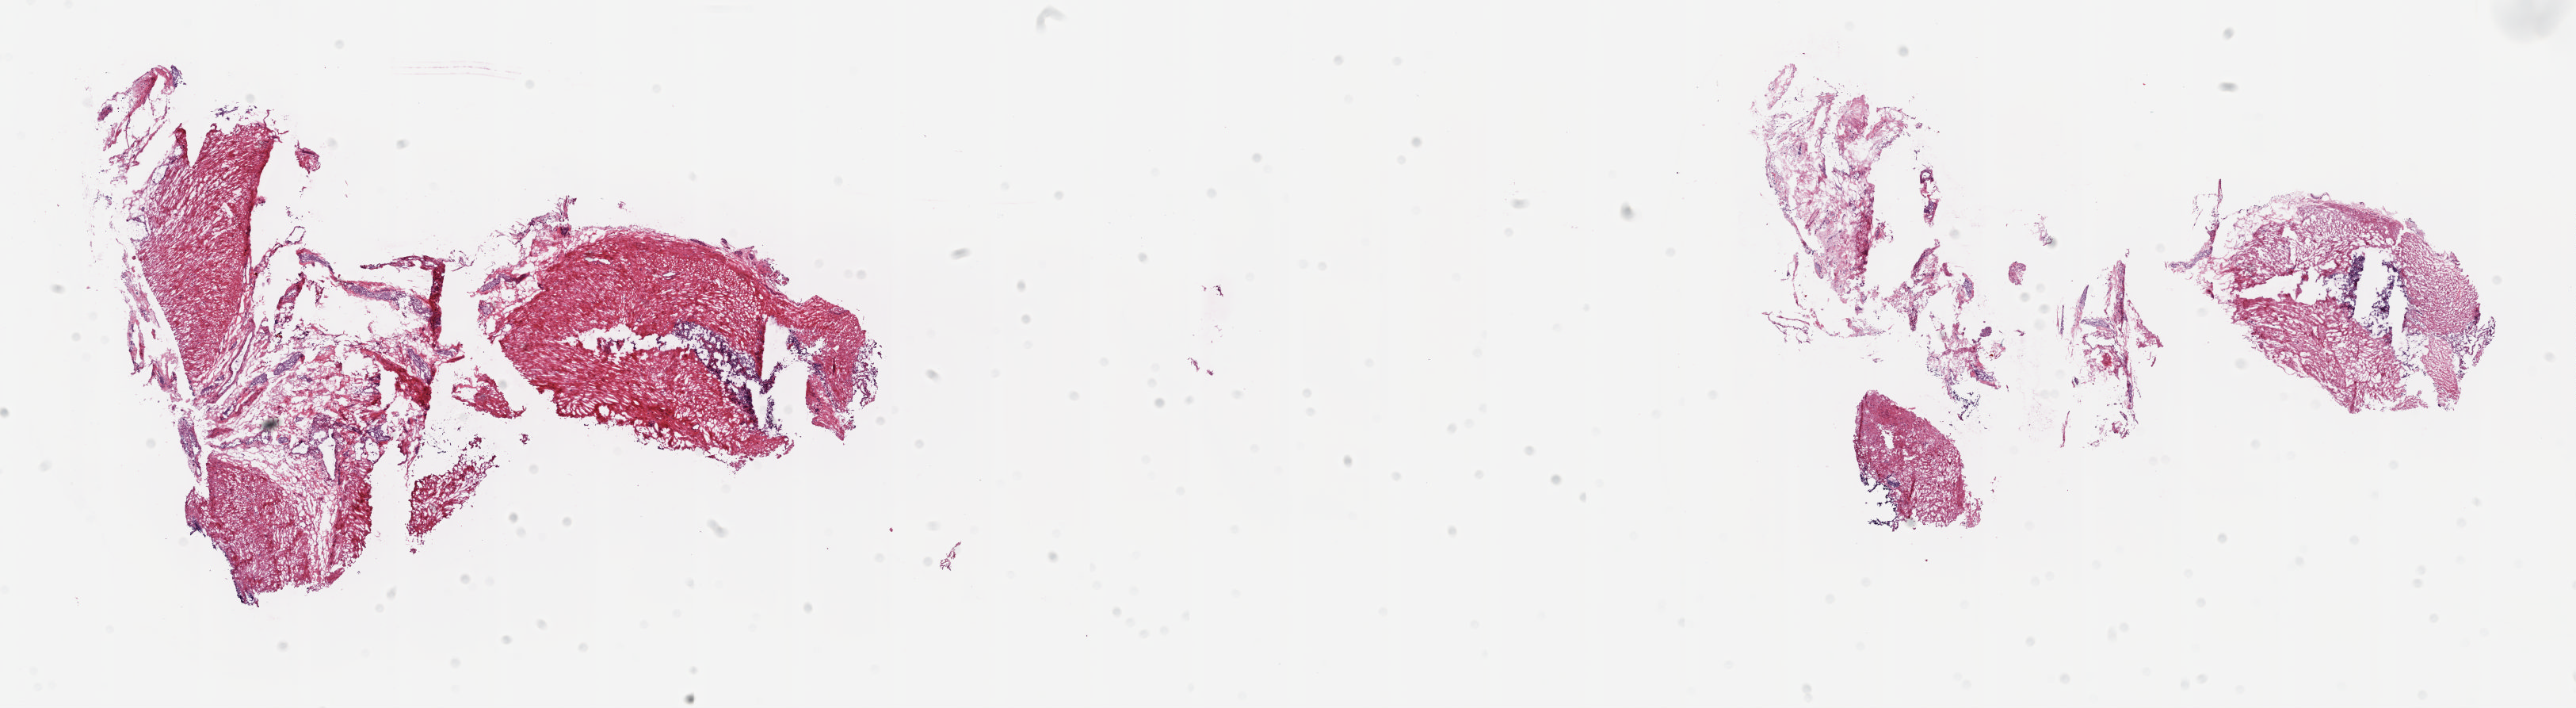
Digitized H&E-stained tissue section (whole slide), a low-resolution overview of the entire scanned area, about 25.8 x 7.1 mm (acquisition: 20x scan). Frozen section. Sample: solid tissue normal (non-tumour tissue), prostate. Male patient; age at initial diagnosis 68 years. Slide review estimates, as recorded: tumour cells 0%, tumour nuclei 0%, normal cells 4%, stromal cells 96%, necrosis 0%. Inflammatory infiltration, as recorded: lymphocyte infiltration 5%, monocyte infiltration 0%, neutrophil infiltration 0%.
- this section: solid tissue normal (non-tumour) sample from the same patient
- patient diagnosis: Adenocarcinoma, NOS (prostate gland)